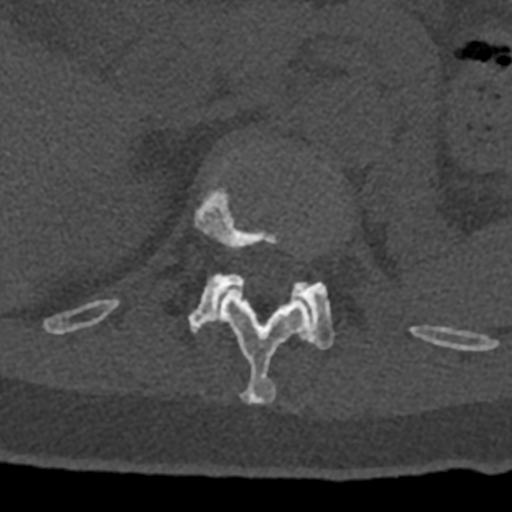
CT including the spine, one axial slice; reconstruction kernel Br40s/3; bone window (W 1800 / L 400 HU); 512 × 512 image matrix, field of view 160 × 160 mm. Patient: male, 74 years. From the clinical record (not read from this slice): primary cancer: renal; vertebrae with lytic lesions (as recorded): T10, L1, L2, L3, L4, L5.
Annotated regions visible in this slice (semi-automatic segmentation, software-assisted and operator-edited):
- L1 vertebra: box from (x=188, y=273) to (x=334, y=350) px
- T12 vertebra: (x=70, y=162)–(x=432, y=404)